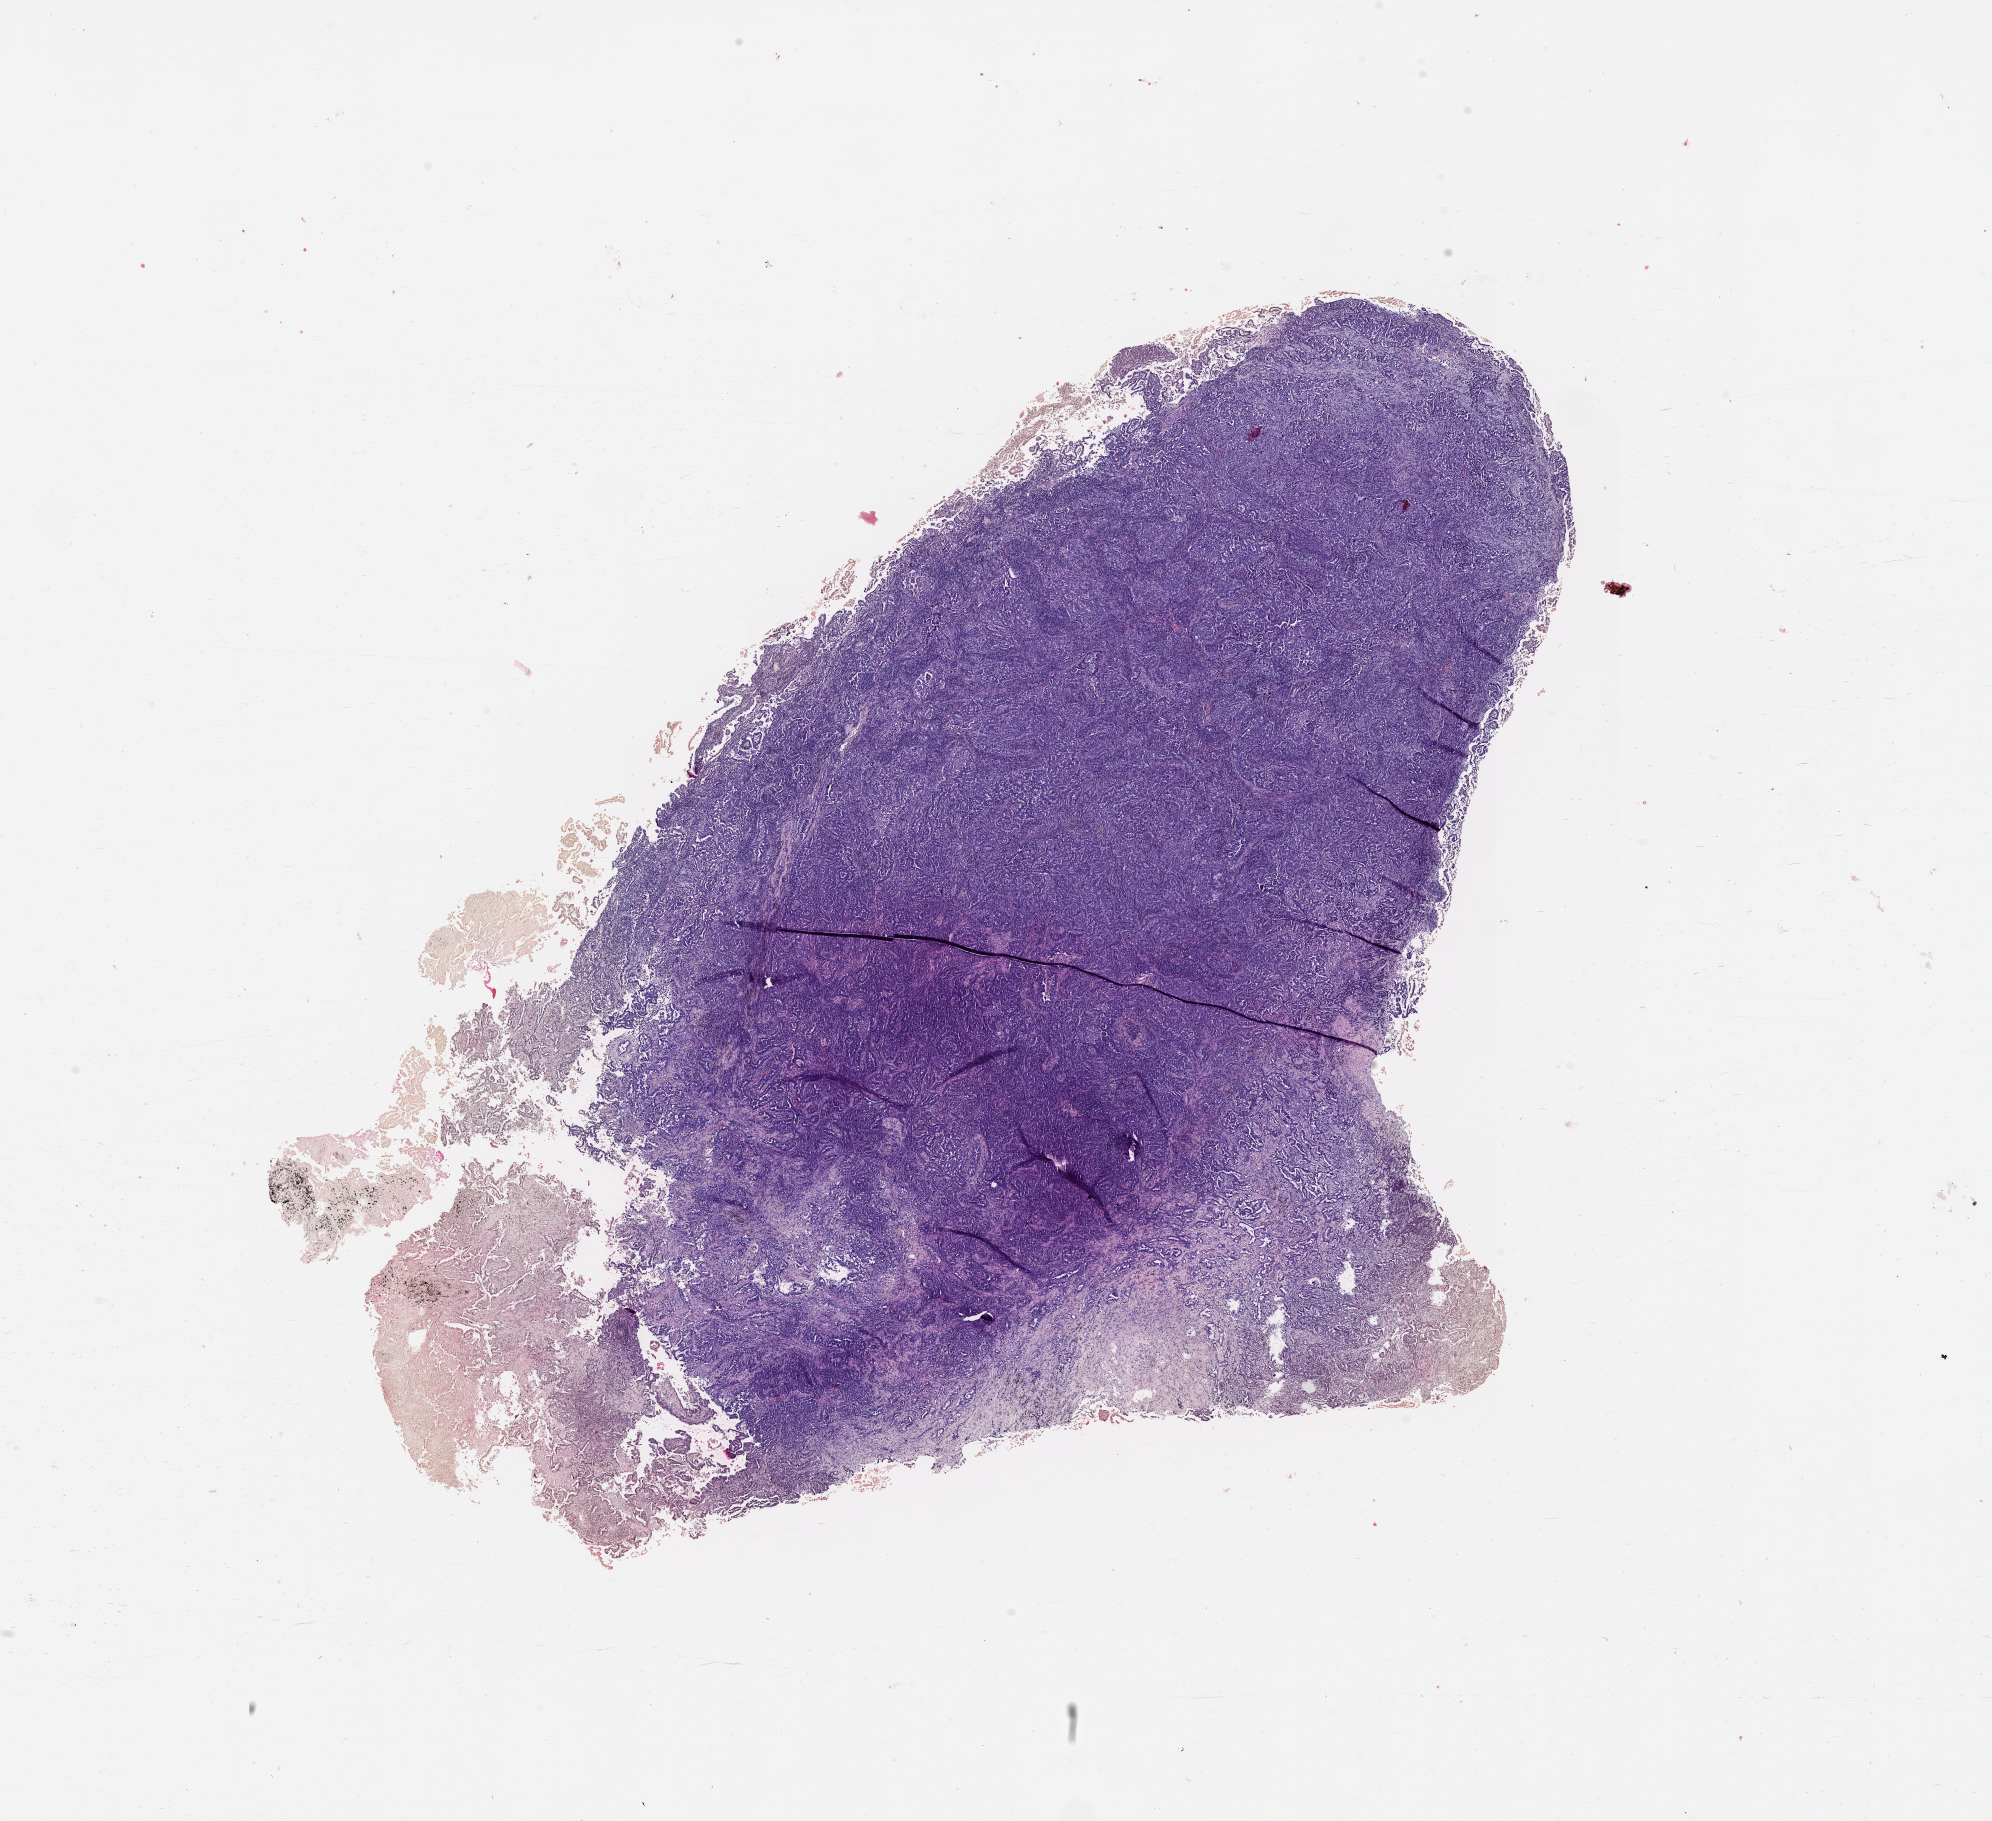
H&E whole-slide image — whole scanned area (about 16.0 x 14.7 mm, from a 20x scan) shown as a low-resolution overview. Tumour tissue sample, lung. 68-year-old male patient. Histologic grade: G1 (well differentiated).
AJCC pathologic stage: IB. Histologic diagnosis: Adenocarcinoma, NOS.